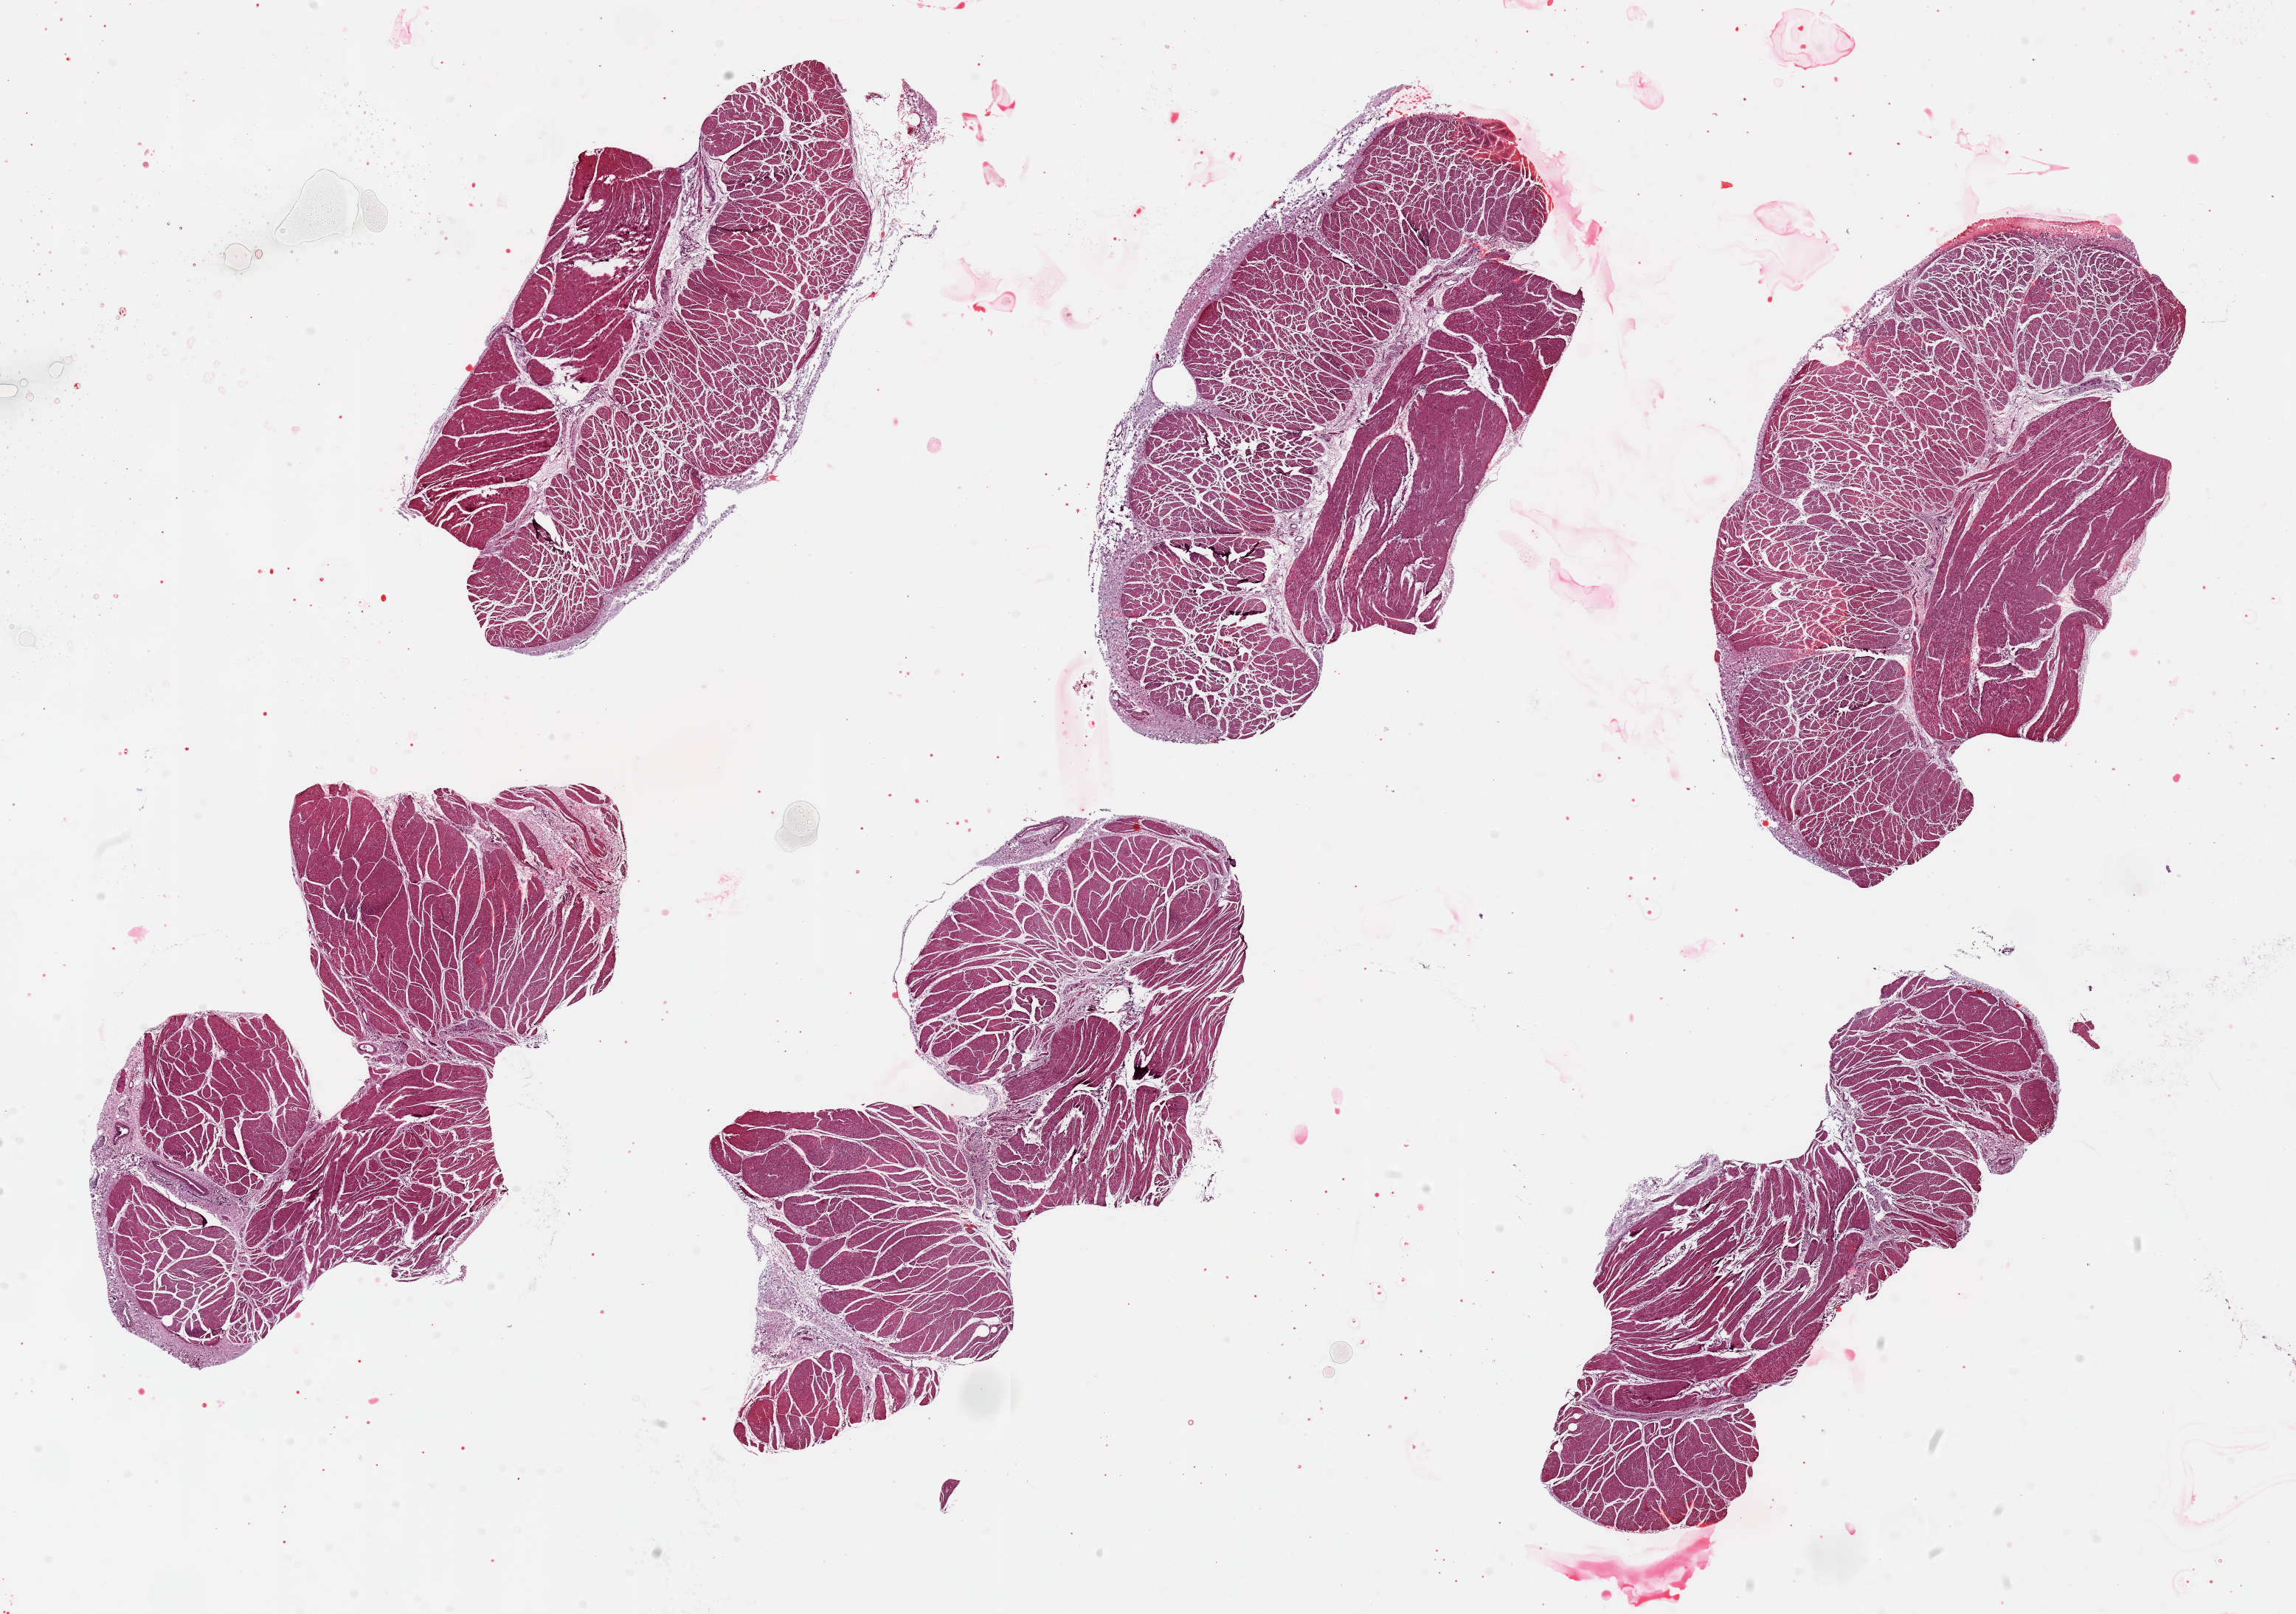
Digitized haematoxylin and eosin-stained section — shown as a low-resolution overview of the whole scanned area (about 24.6 x 17.3 mm, slide scanned at 20x), PAXgene-fixed paraffin-embedded (PFPE) section, section of esophageal muscle (target tissue), tissue donor sample. Donor sex: female.
Review note (as recorded): 6 pieces, up to 8x4mm; all have well trimmed muscle.